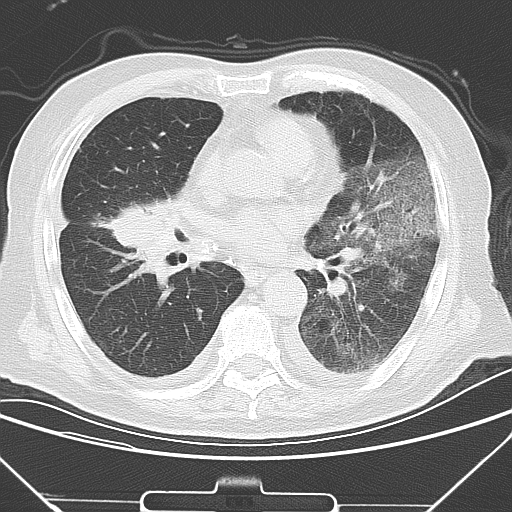
Chest CT, one axial slice; position 16 of 43 along the scan axis; lung window (W 1500 / L -600 HU); 512 × 512 image matrix, field of view 343 × 343 mm. Patient: male, 85 years. Case-level facts recorded for this patient, not image findings: clinical TNM (as recorded): T4 N3 M2.
Annotated regions visible in this slice (rectangle marked by the reading radiologist):
- lung tumour (recorded histology: squamous cell carcinoma): box from (x=97, y=191) to (x=178, y=288) px